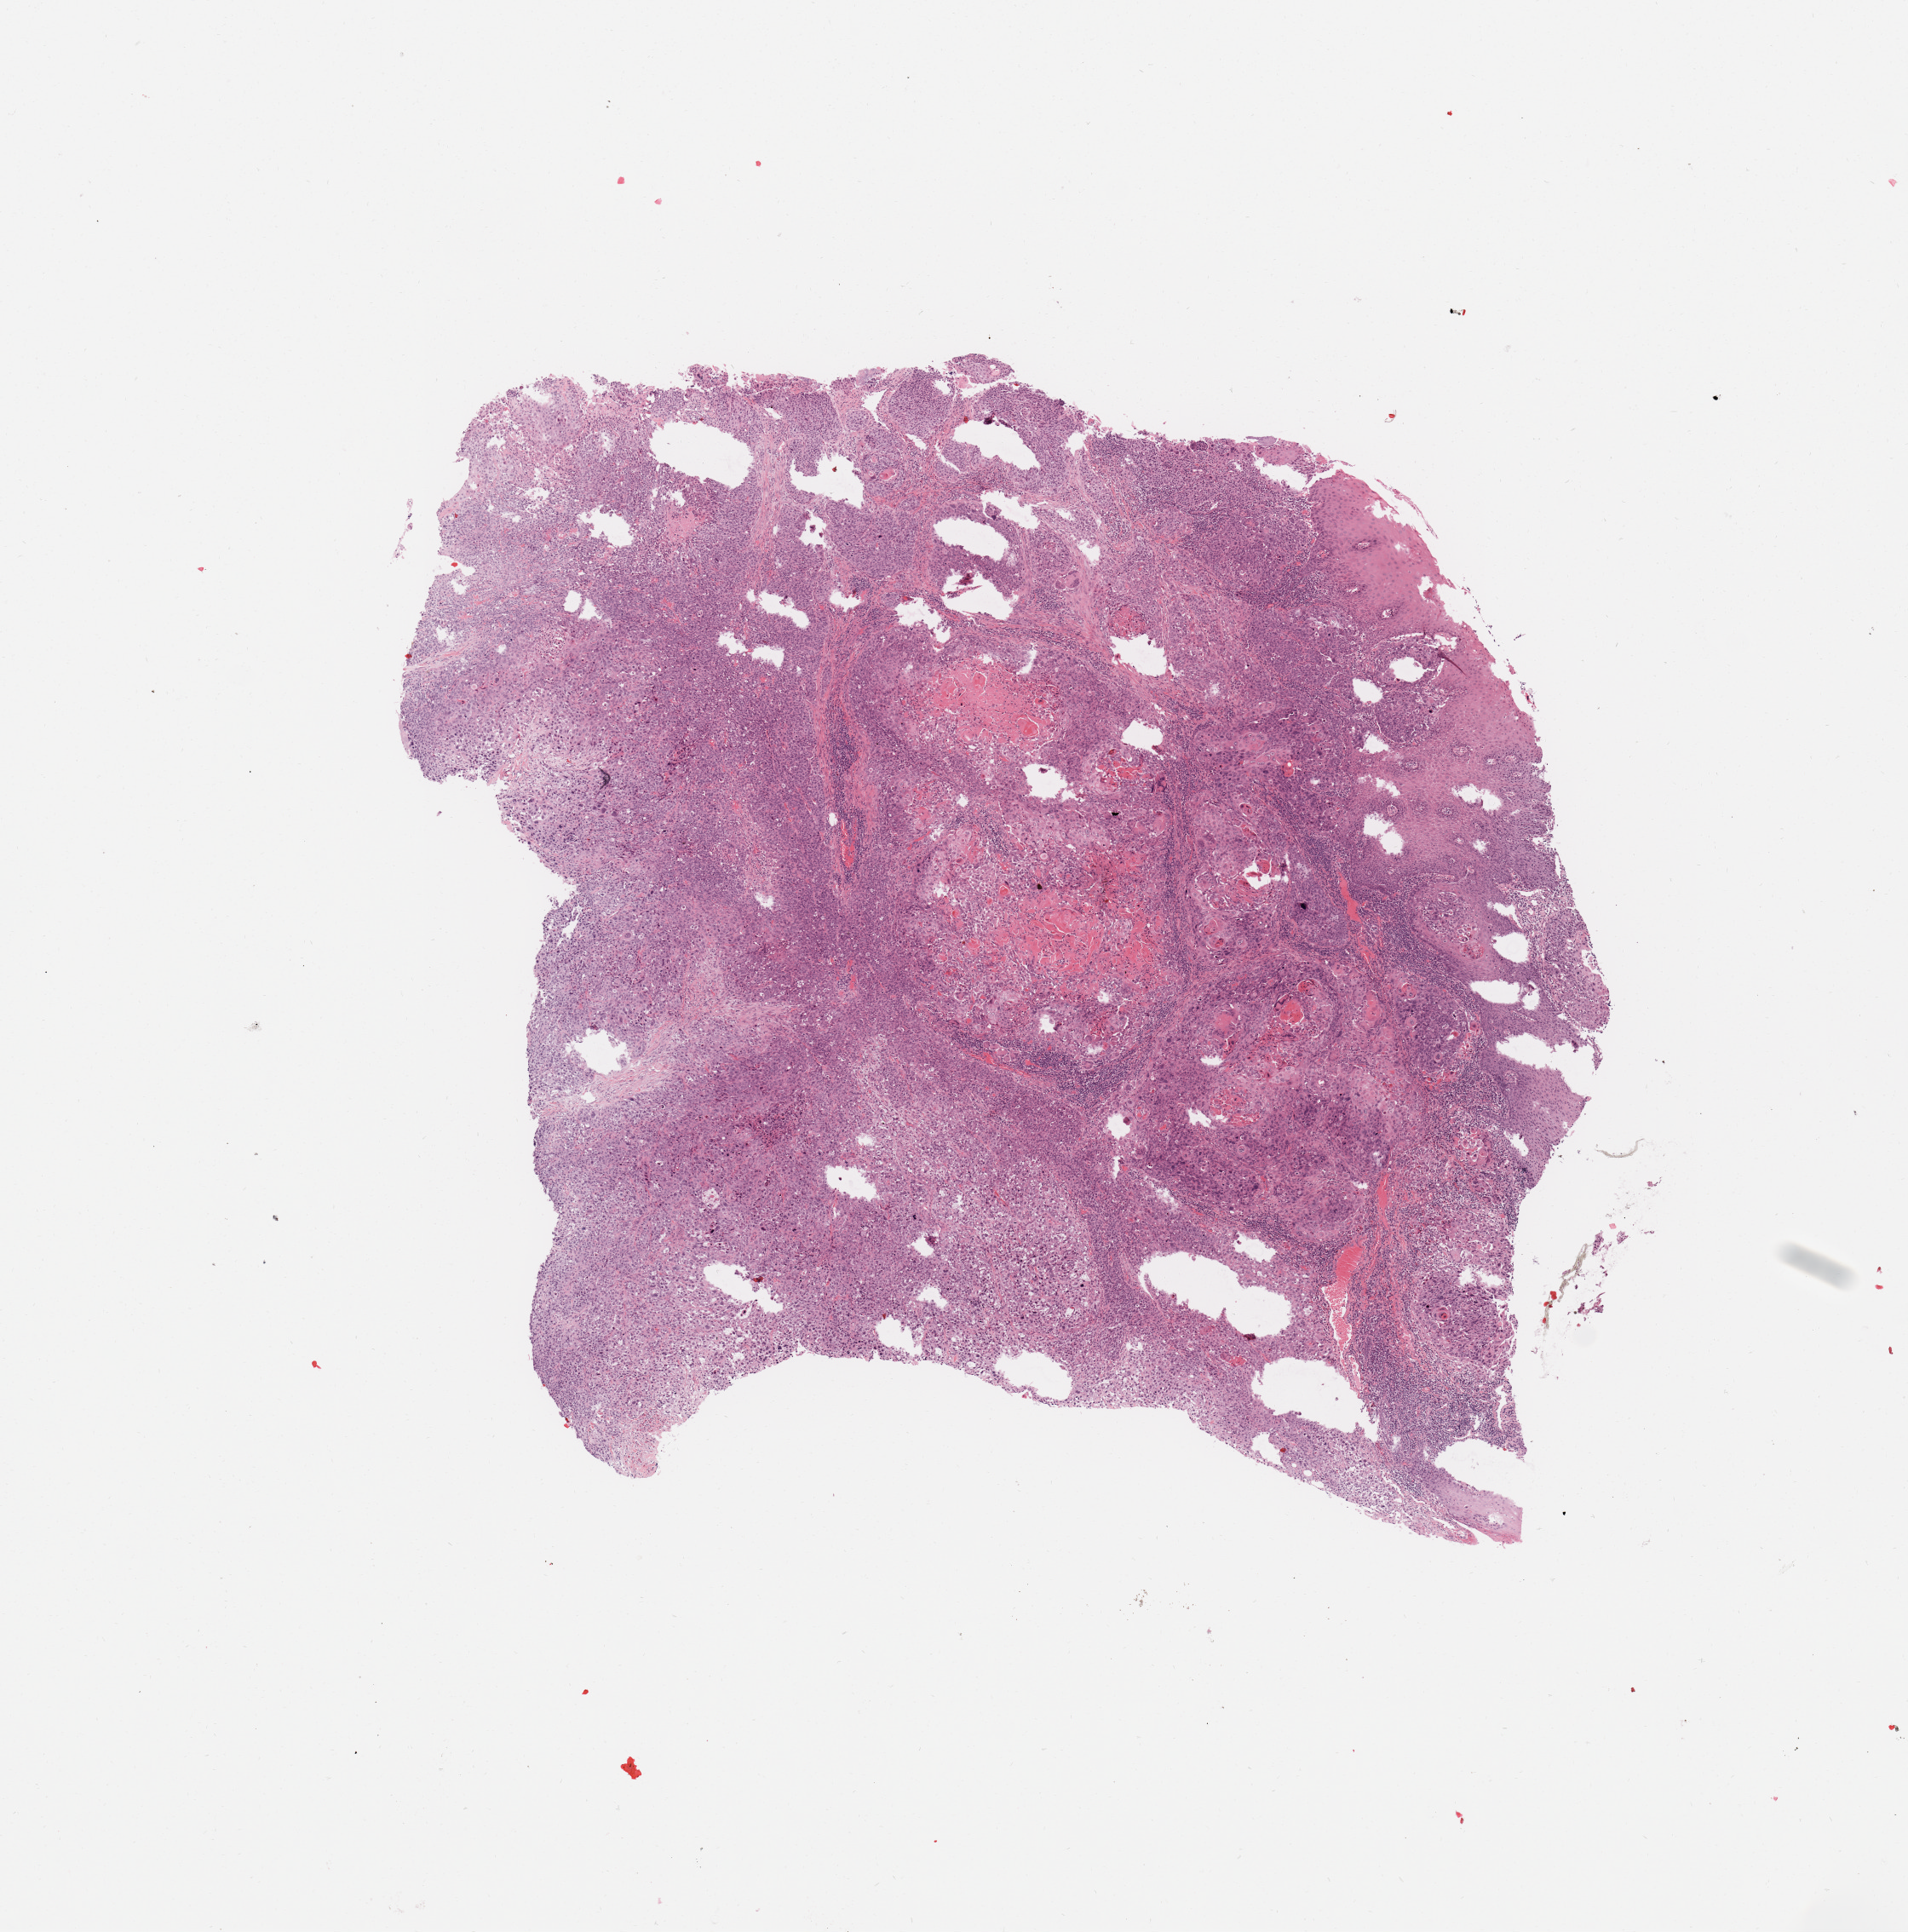
Digitized H&E tissue section (whole slide), shown as a low-resolution overview of the whole scanned area (about 8.9 x 9.0 mm), tumour tissue sample, sampled site: larynx. Patient: male, age 65 years. Histologic grade: G1 (well differentiated). Slide review estimates, as recorded: tumour nuclei 85%, necrosis 5%.
• AJCC pathologic stage: IVA
• primary tumour site (as recorded): larynx
• histologic diagnosis: Squamous cell carcinoma, NOS